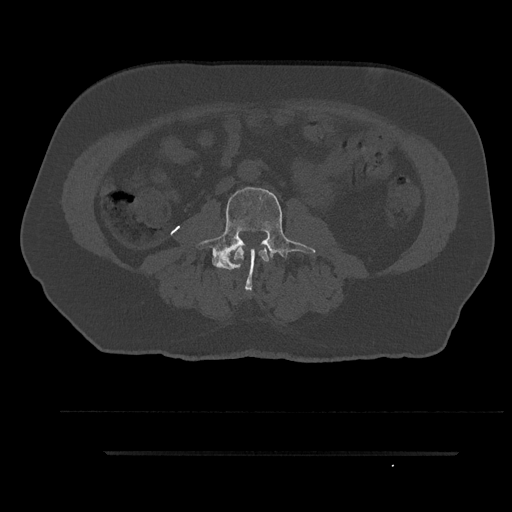
CT including the spine, one axial slice. Slice 49 of 797 in the series (ordered by position). Reconstruction kernel Br40s/3. 120 kVp. Bone window (W 1800 / L 400 HU). 0.5 mm slice thickness. 512 × 512 image matrix, field of view 432 × 432 mm. Patient: male, 63 years. From the clinical record (not read from this slice): primary cancer: renal.
Annotated regions visible in this slice (semi-automatically segmented with operator editing):
- L2 vertebra: bounding box <234,247,269,269> (left, top, right, bottom; pixels)
- L3 vertebra: <196,185,316,291>